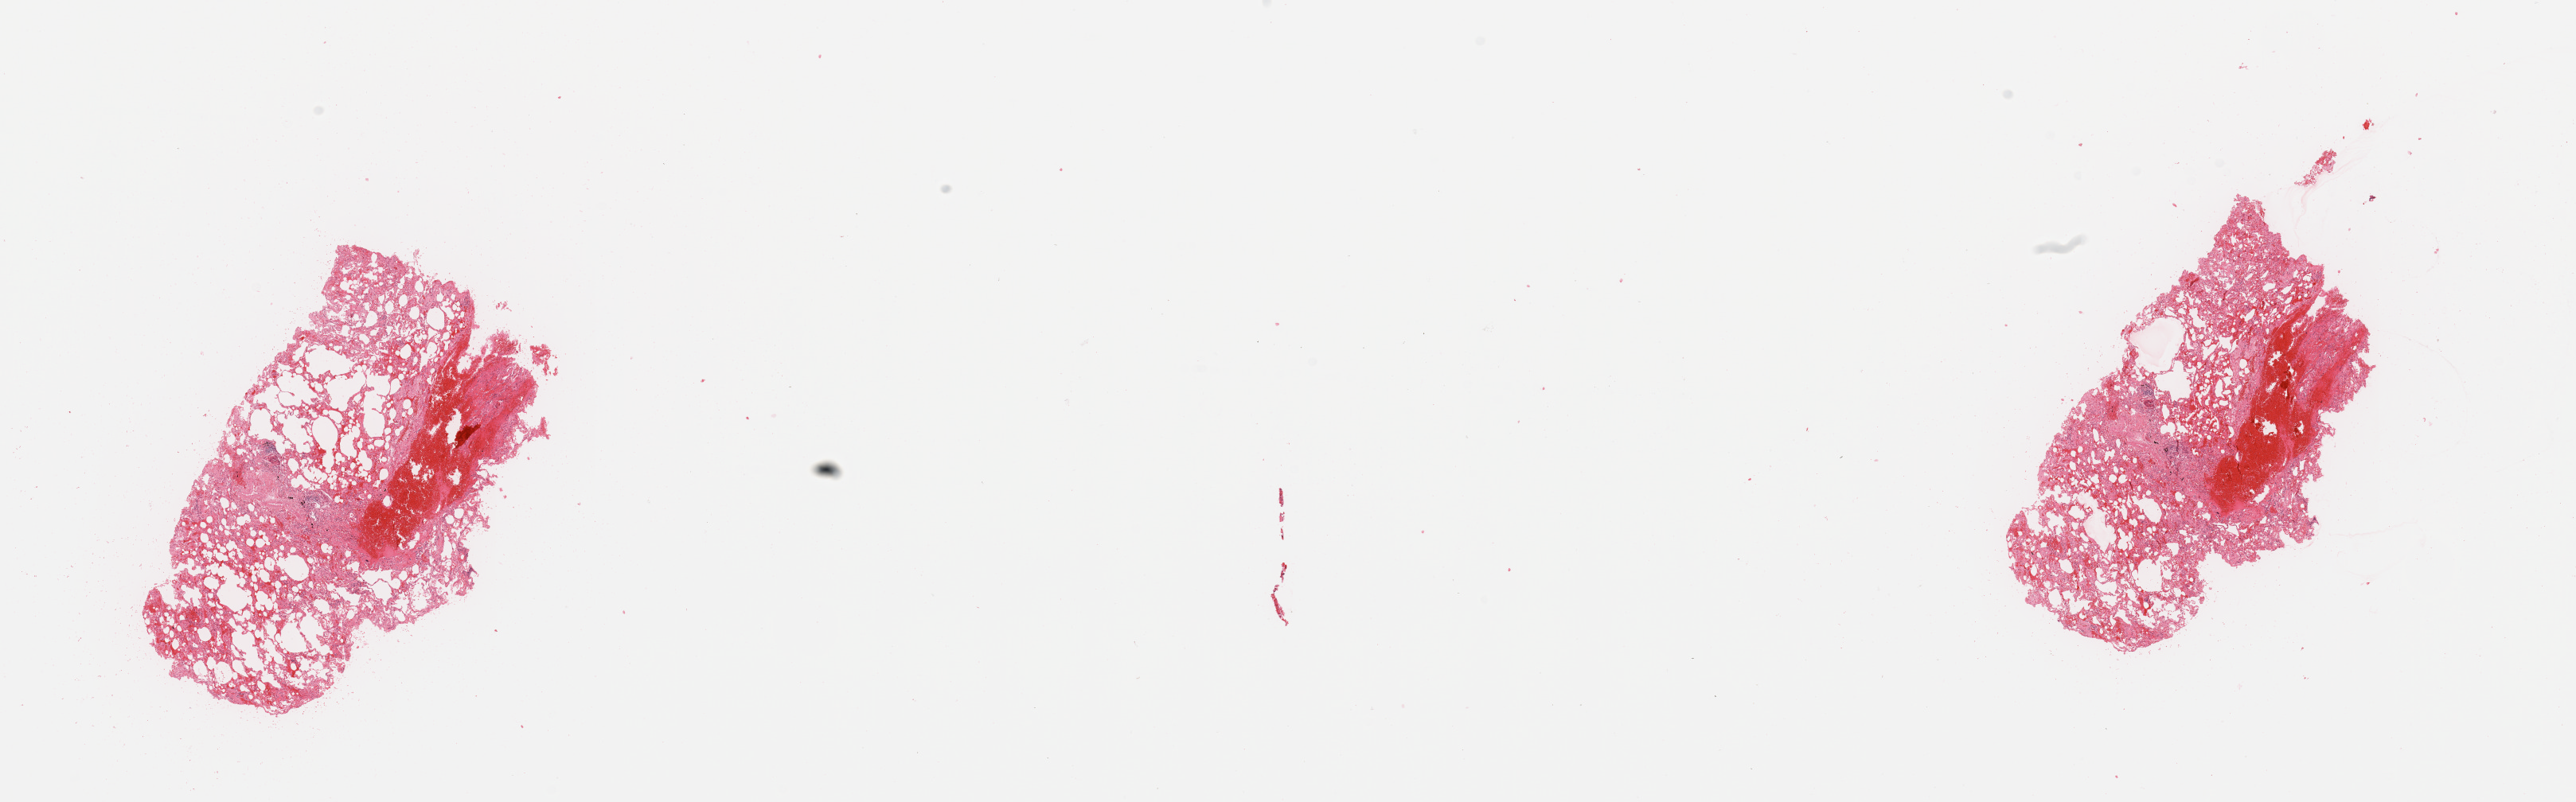
Whole-slide histology image, H&E-stained — a low-resolution overview of the entire scanned area, about 25.6 x 8.0 mm; normal (non-tumour) tissue sample, sampled site: lung. Female, 72 y/o.
This section: normal (non-tumour) tissue from the same patient. Patient diagnosis: Adenocarcinoma, NOS.